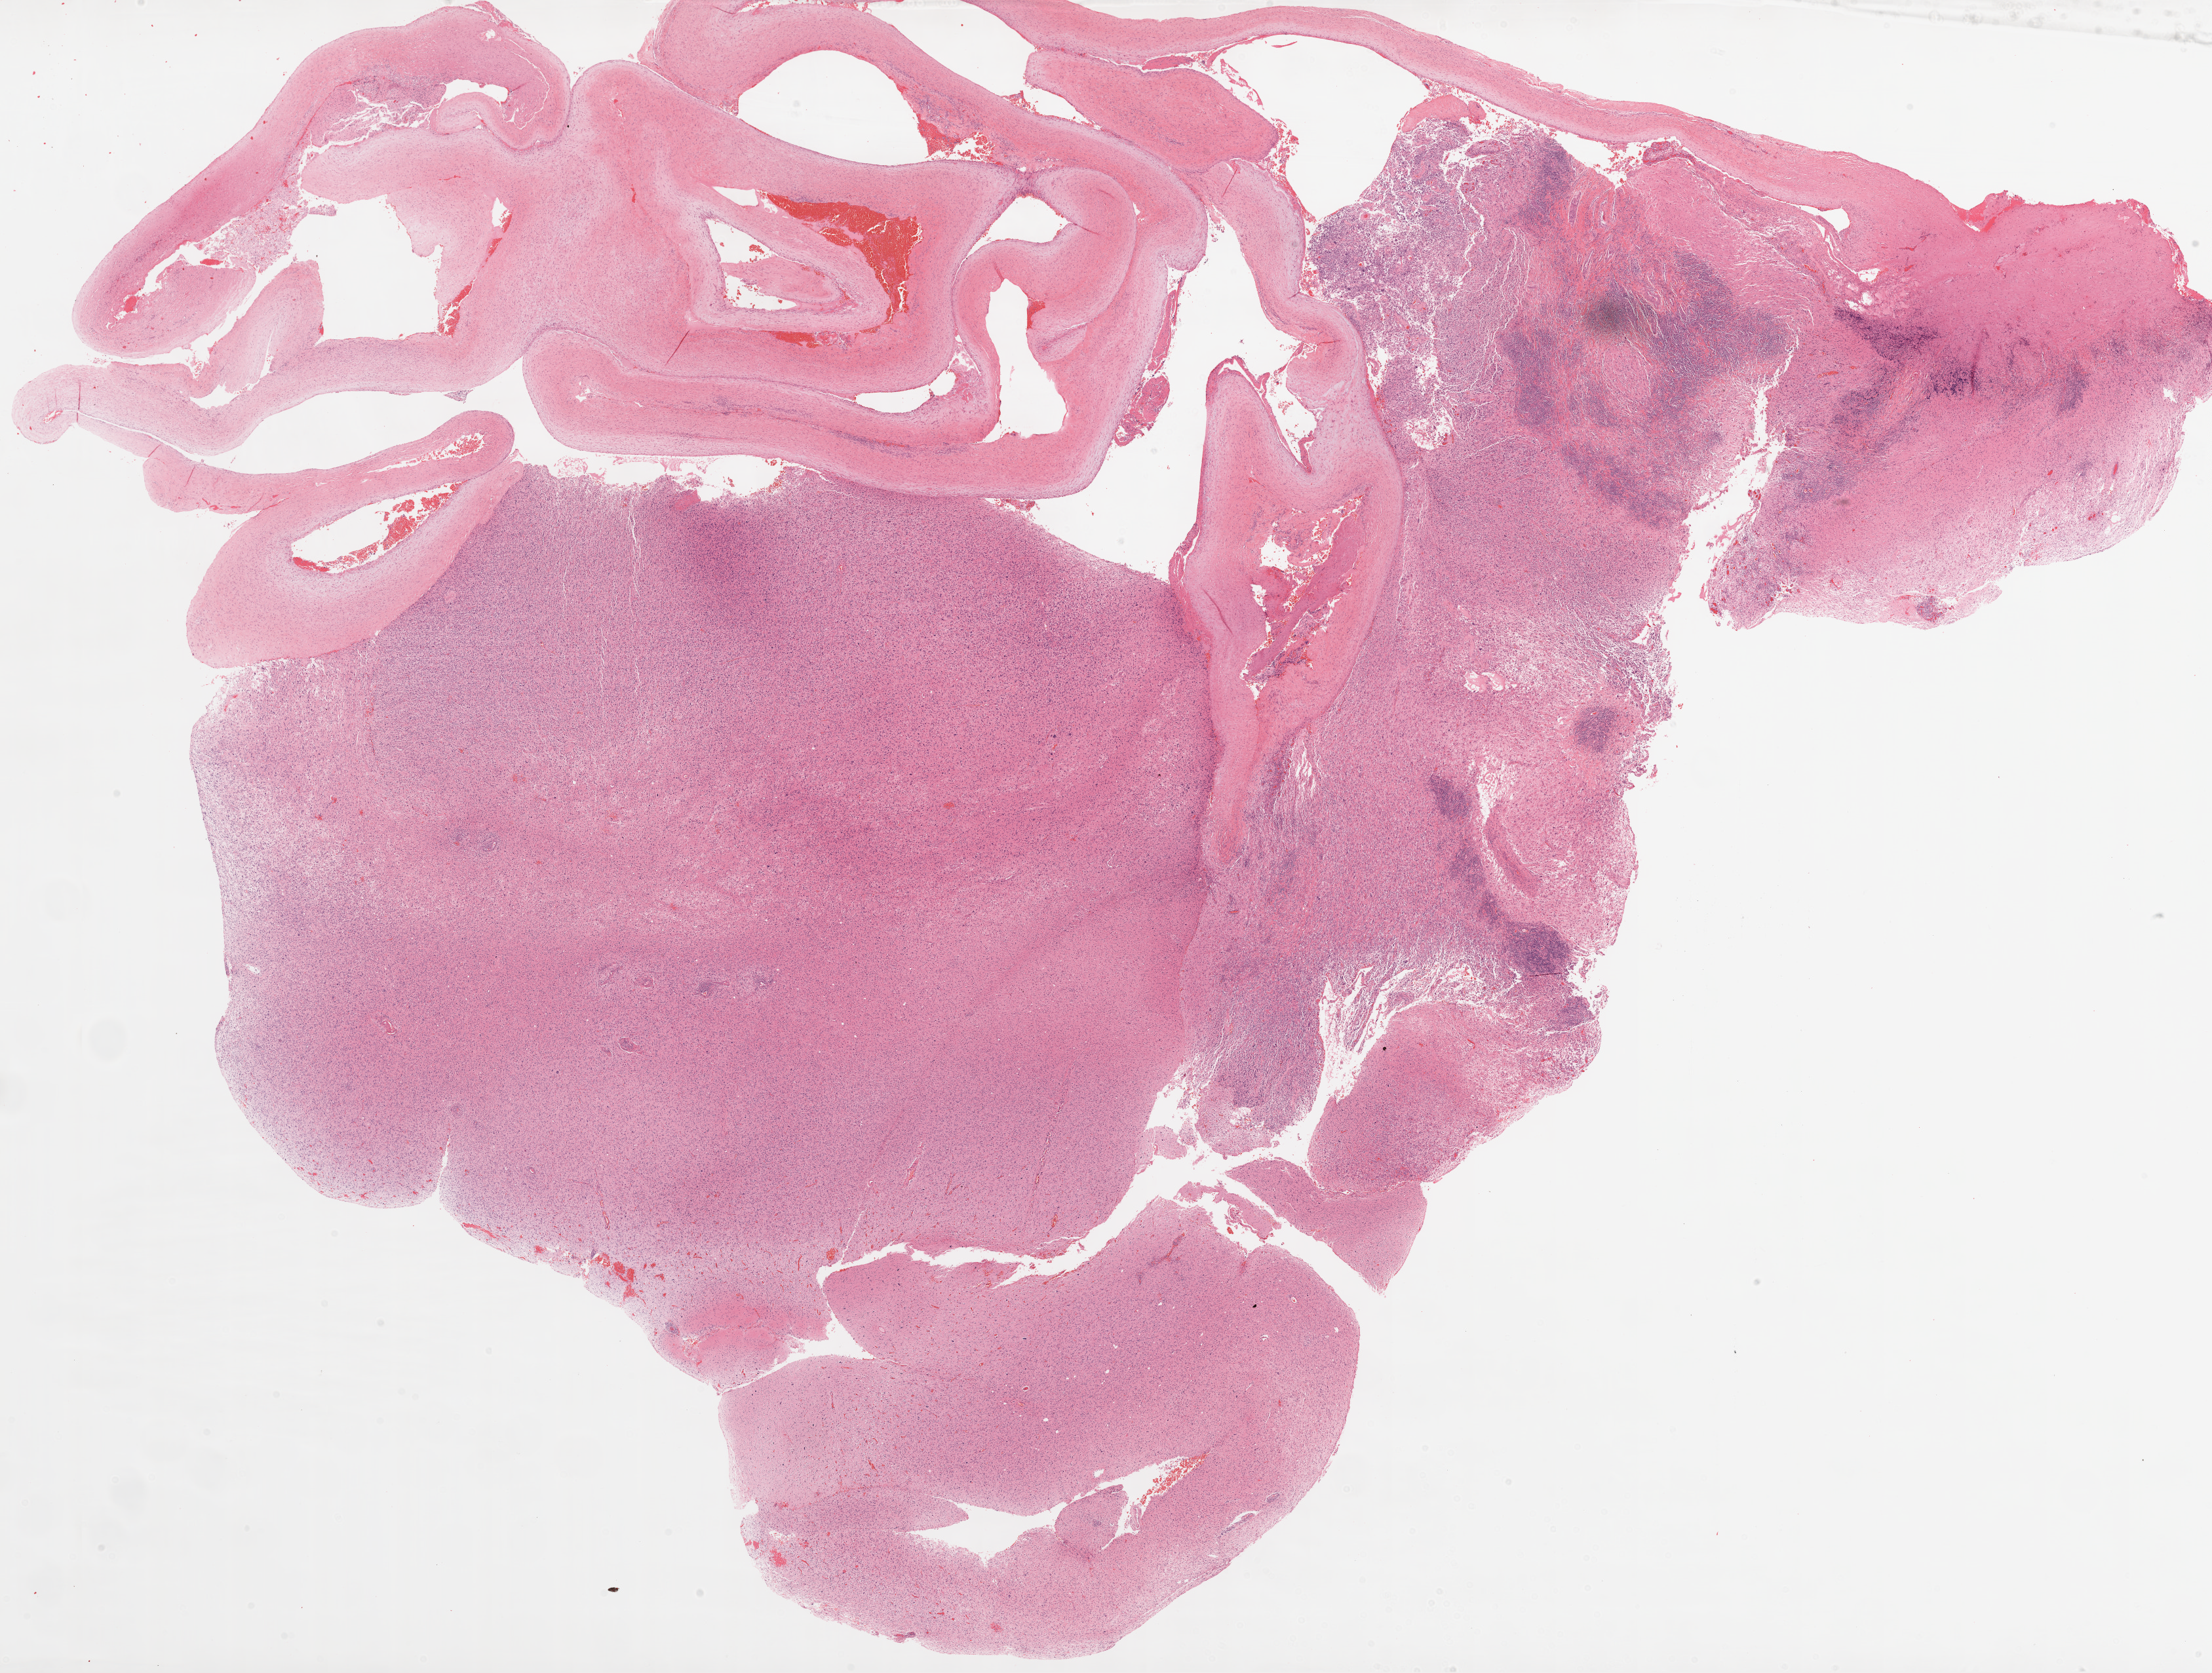
Whole-slide histology image, H&E, a low-resolution overview of the entire scanned area, about 27.1 x 20.5 mm. Formalin-fixed paraffin-embedded (FFPE) diagnostic section. Sample: primary tumour, brain. Female, age 20 years at initial diagnosis.
- diagnosis: Glioblastoma